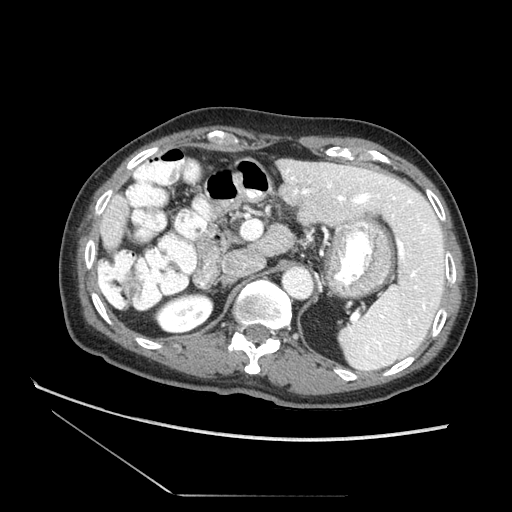
Contrast-enhanced abdominal CT (liver protocol), one axial slice; slice 47 of 73 in the series (ordered by position); reconstruction kernel STANDARD; soft-tissue window (W 400 / L 40 HU); 2.5 mm slice thickness; 512 × 512 image matrix. Case-level facts recorded for this patient, not image findings: diagnosis: hepatocellular carcinoma (patient treated with transarterial chemoembolisation; whether this scan precedes or follows treatment is not stated here); TNM stage (as recorded): Stage-II; Child-Pugh class: A; tumour differentiation: moderately differentiated; tumour nodularity: multinodular.
Structures marked on this image (semi-automatic segmentation, software-assisted and operator-edited):
- liver parenchyma outside the tumour (the mass and vessels are separate outlines, so this box may not span the whole liver): bounding box (x1, y1, x2, y2) in pixels: (106, 198, 128, 241)